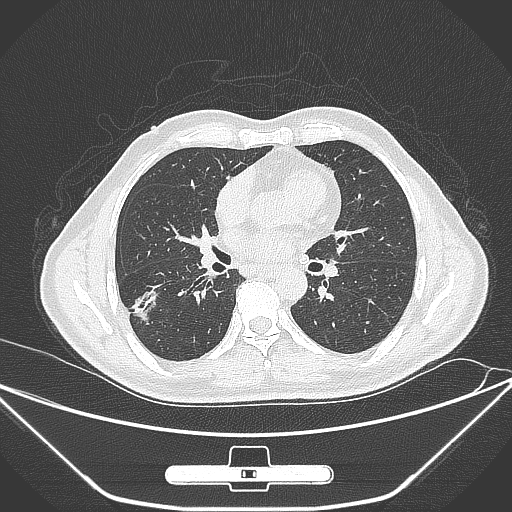
Chest CT, one axial slice. Lung window (W 1500 / L -600 HU). 1 mm slice thickness. 512 × 512 image matrix. Patient: male, 71 years. Case-level facts recorded for this patient, not image findings: clinical TNM (as recorded): T1c N0 M0; histopathological grade: G2.
Annotated regions visible in this slice (bounding box drawn by a radiologist):
- lung tumour (recorded histology: adenocarcinoma): box from (x=131, y=286) to (x=160, y=328) px